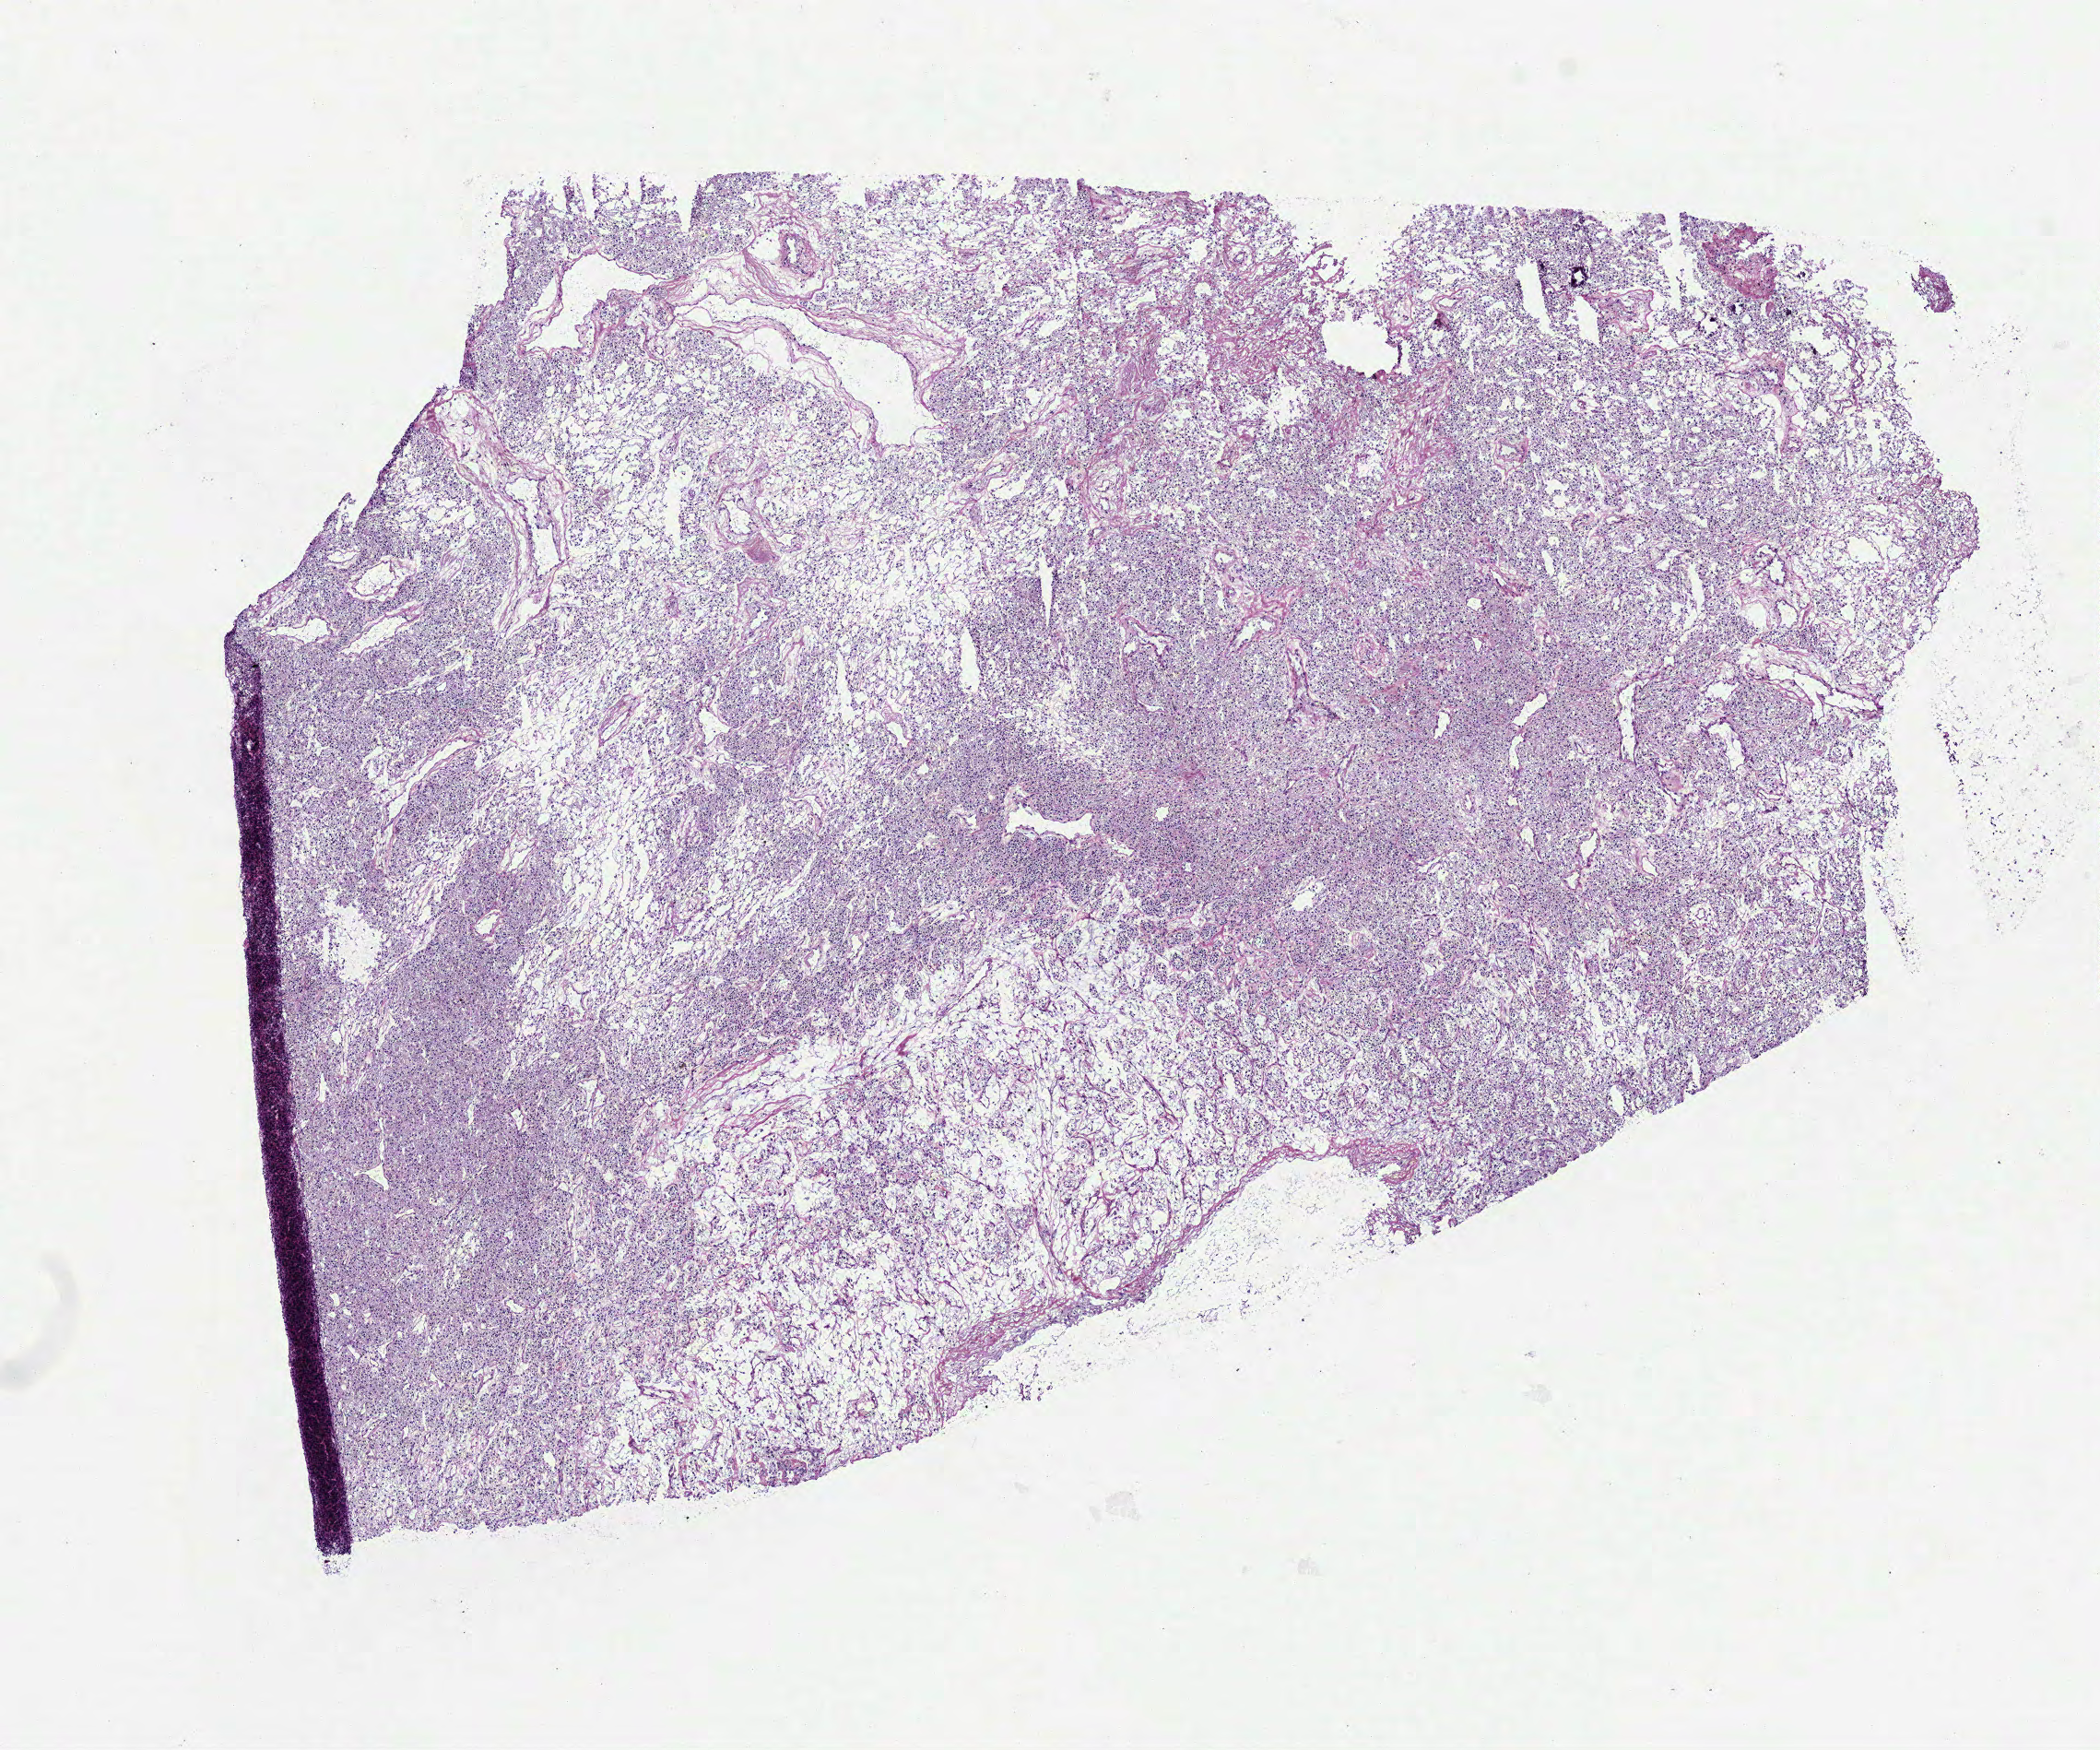
H&E whole-slide image, shown as a low-resolution overview of the whole scanned area (about 9.2 x 7.7 mm, slide scanned at 40x). Frozen section from the top of the tissue portion. Primary tumour sample from the kidney. Male, age 81 years at initial diagnosis. Histologic grade: G3 (poorly differentiated). Composition of this section per pathologist review: tumour cells 85%, tumour nuclei 80%, normal cells 0%, stromal cells 15%, necrosis 0%.
AJCC pathologic stage: III (7th edition). Laterality: right. Diagnosis: Clear cell adenocarcinoma, NOS.